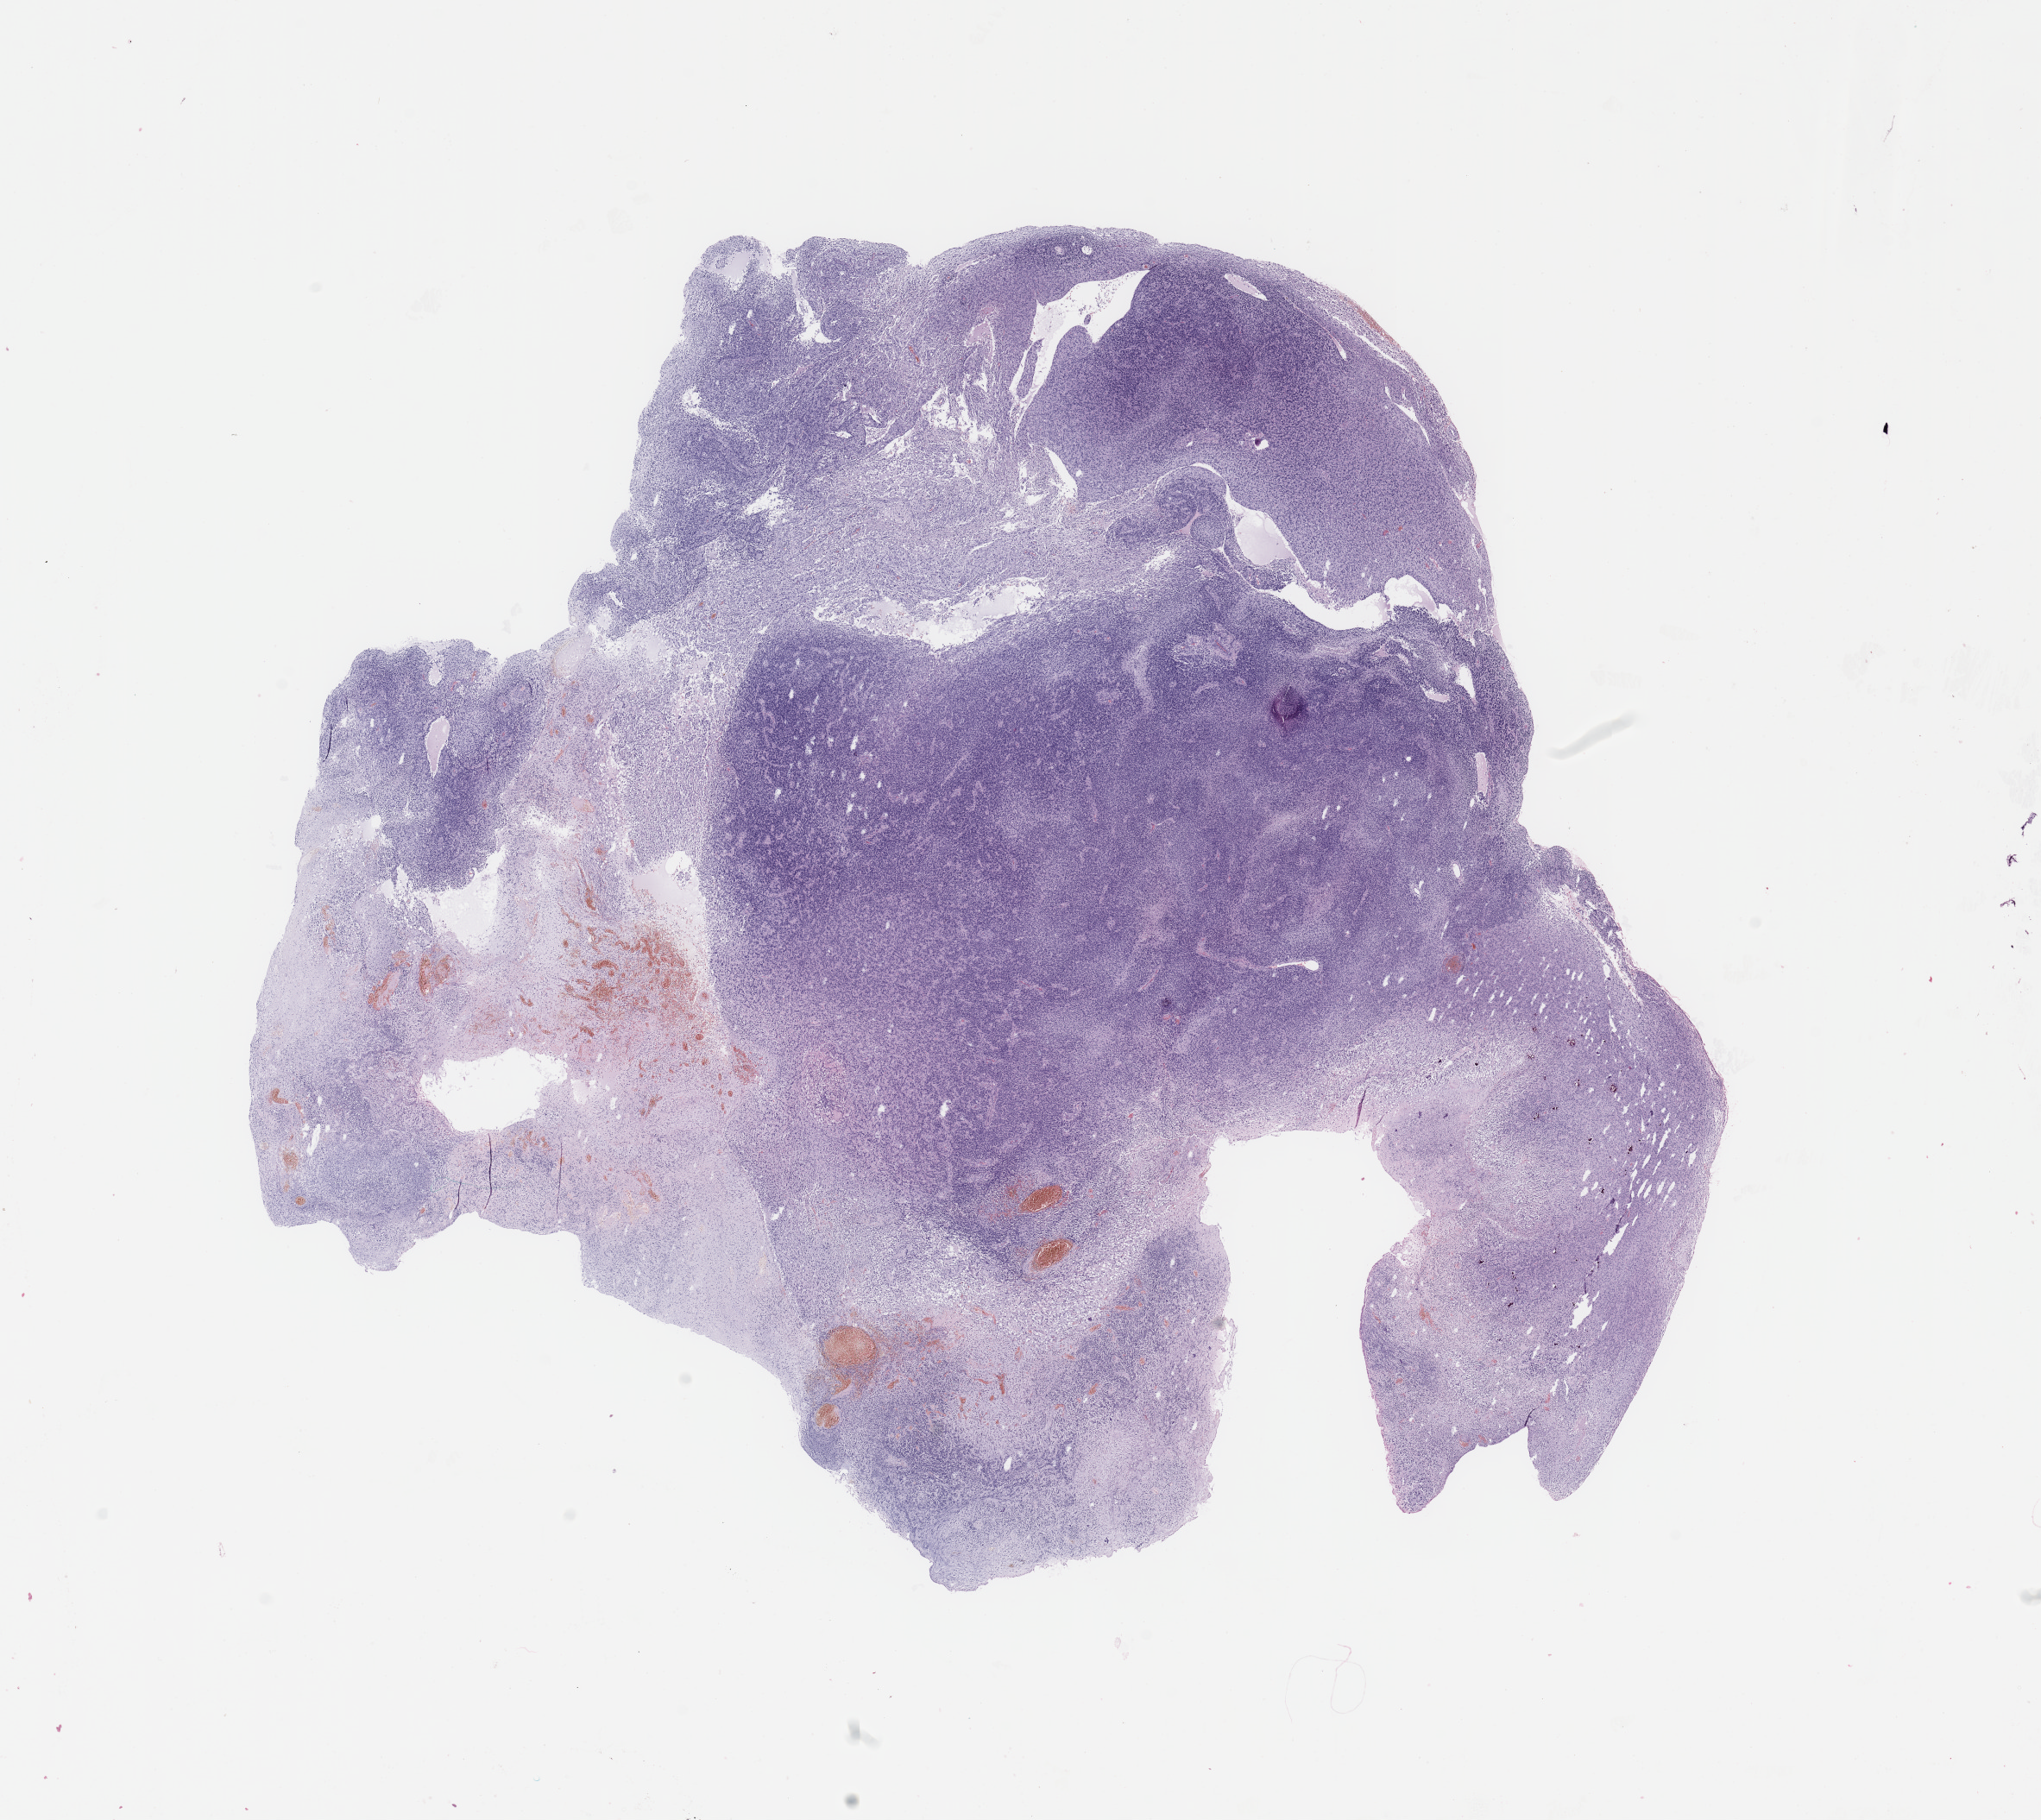
H&E-stained whole-slide image — whole scanned area (about 18.7 x 16.7 mm, acquisition: 20x scan) shown as a low-resolution overview. Tumour tissue sample, brain. Male, 81 y/o.
Primary tumour site (as recorded): temporal lobe. Diagnosis: Glioblastoma.